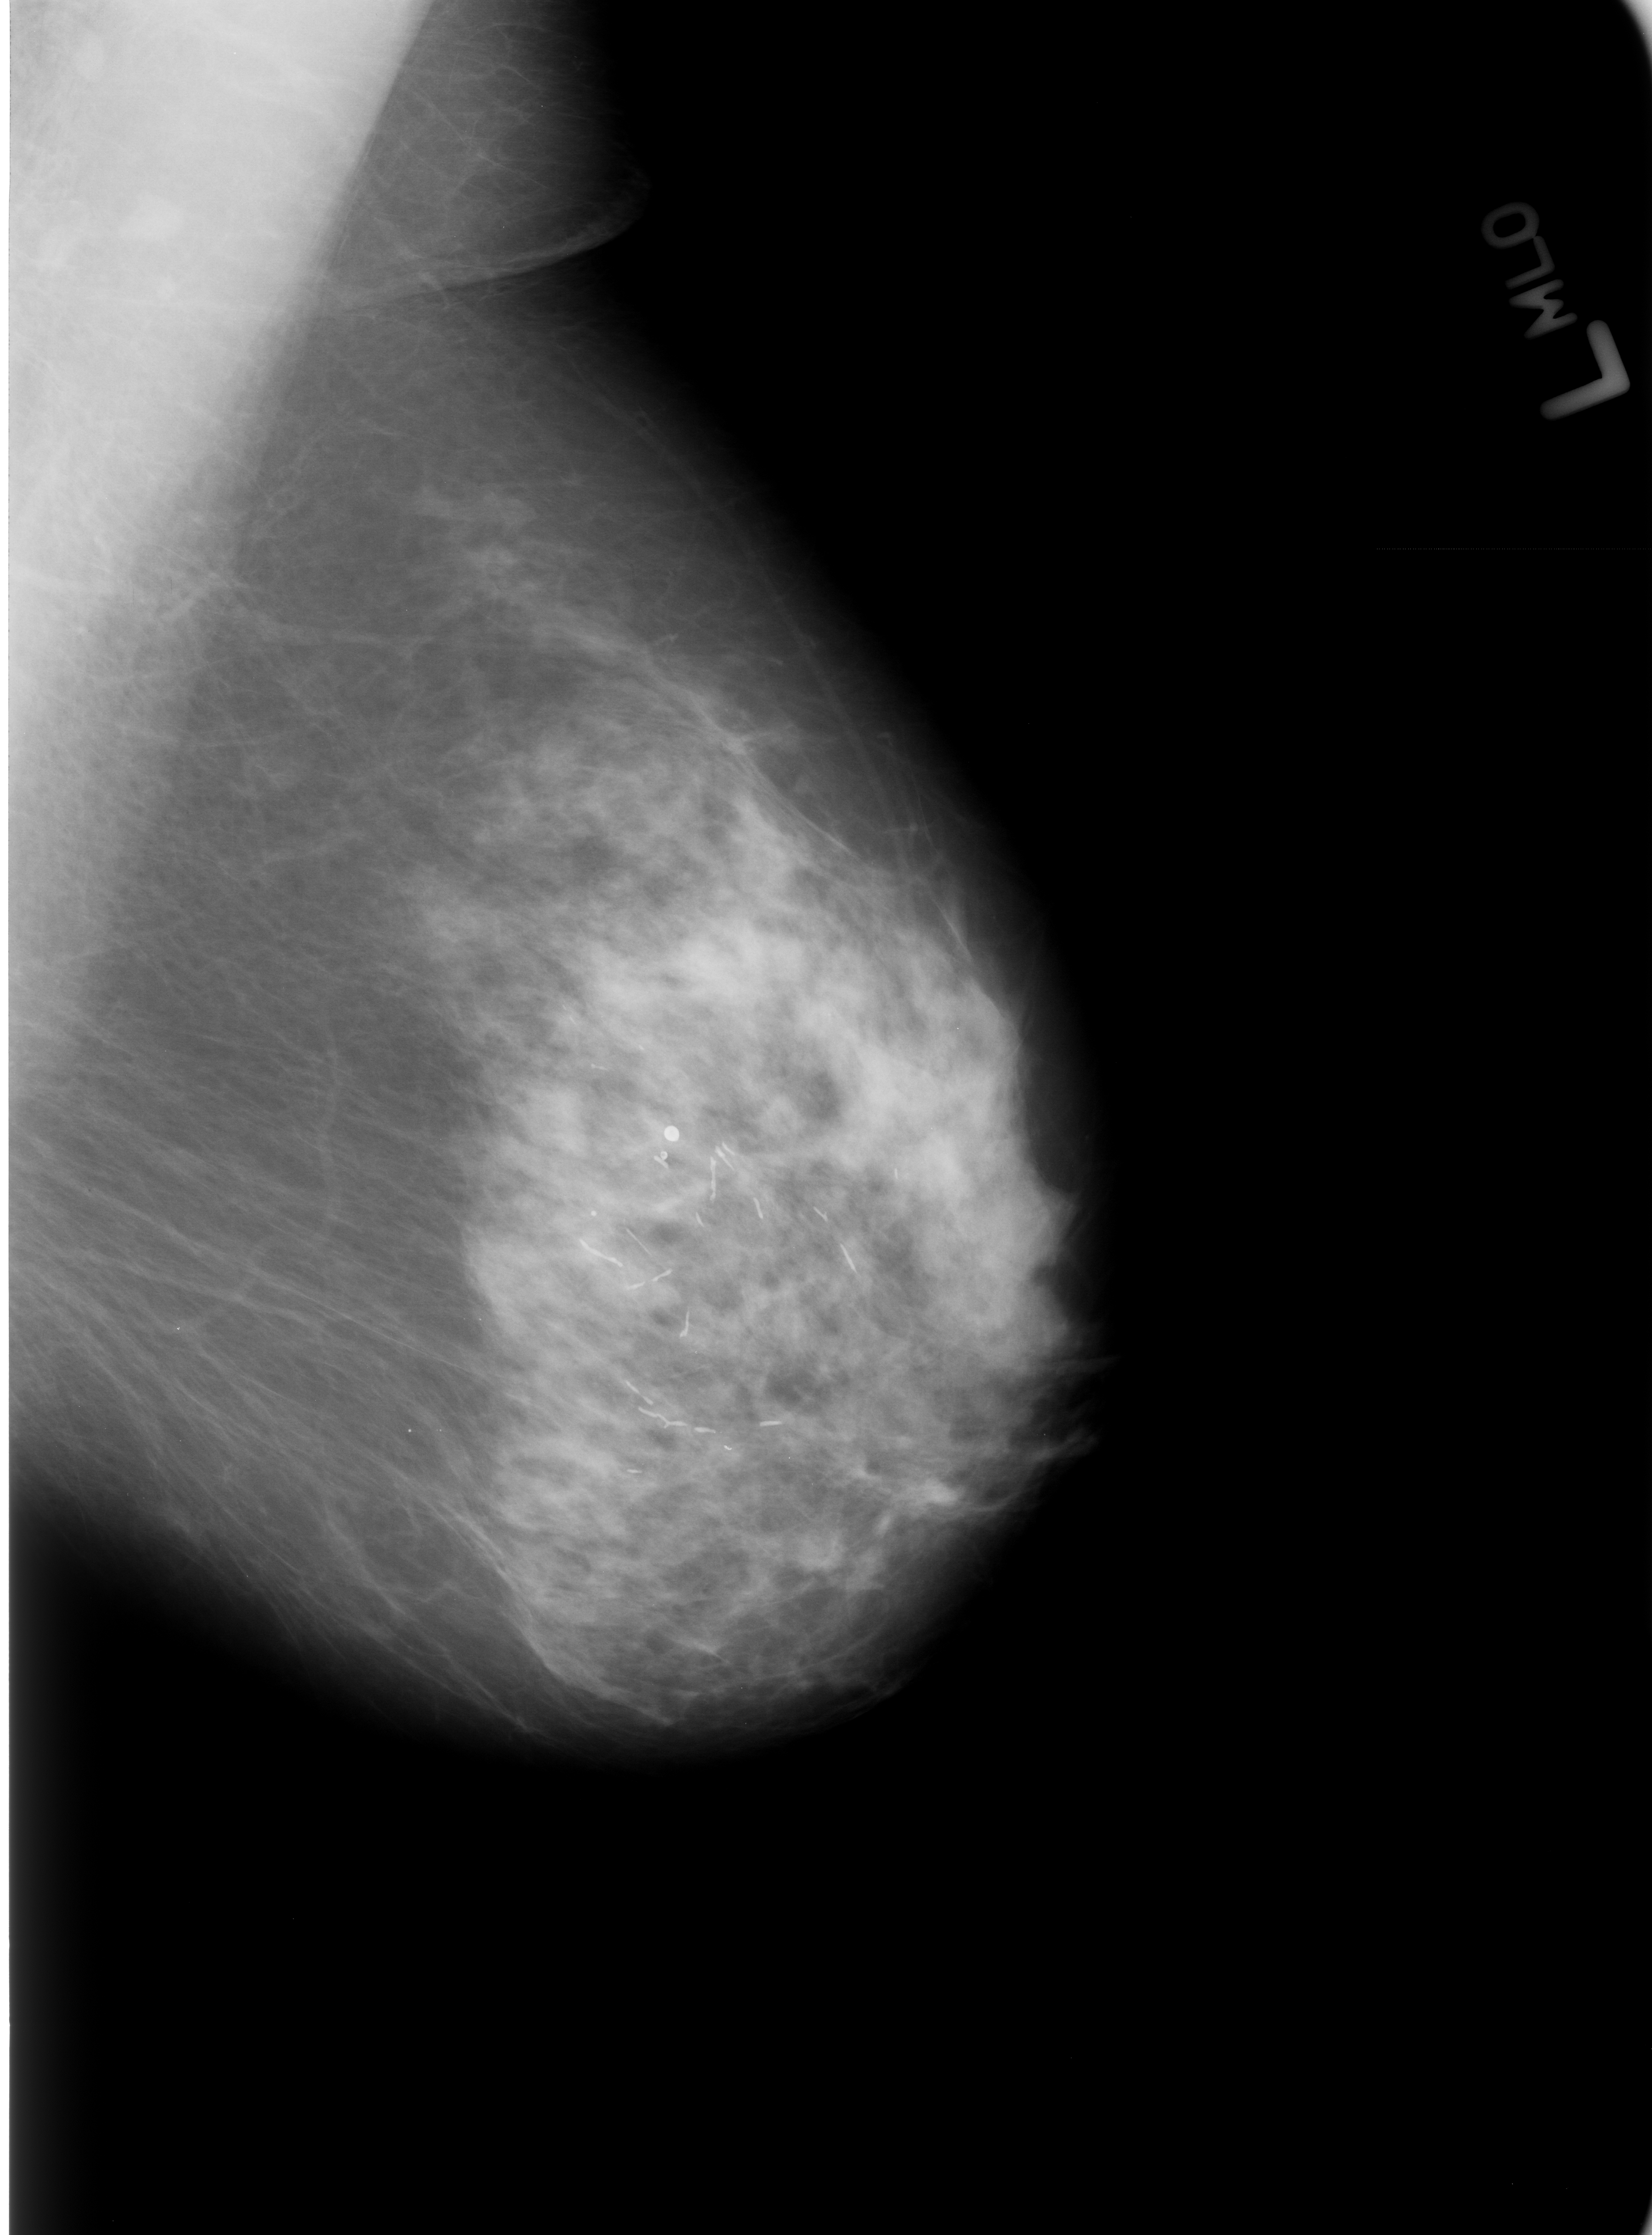
Scanned film-screen mammogram; left breast; MLO view; BI-RADS breast density category 3 (scale 1–4).
Abnormality record for this image: Finding 1 of 5: calcifications, morphology large rodlike / round and regular, distribution regional; BI-RADS assessment category 2; benign without callback (not worked up further). Finding 2 of 5: calcifications, morphology large rodlike / round and regular, distribution regional; BI-RADS assessment category 2; subtlety rating 5 on a 1 (subtle) to 5 (obvious) scale; benign without callback (not worked up further). Finding 3 of 5: calcifications, morphology large rodlike / round and regular, distribution regional; BI-RADS assessment category 2; subtlety rating 5 on a 1 (subtle) to 5 (obvious) scale; benign without callback (not worked up further). Finding 4 of 5: calcifications, morphology large rodlike / round and regular, distribution regional; BI-RADS assessment category 2; benign without callback (not worked up further). Finding 5 of 5: calcifications, morphology large rodlike / round and regular, distribution regional; BI-RADS assessment category 2; subtlety rating 5 on a 1 (subtle) to 5 (obvious) scale; benign without callback (not worked up further).